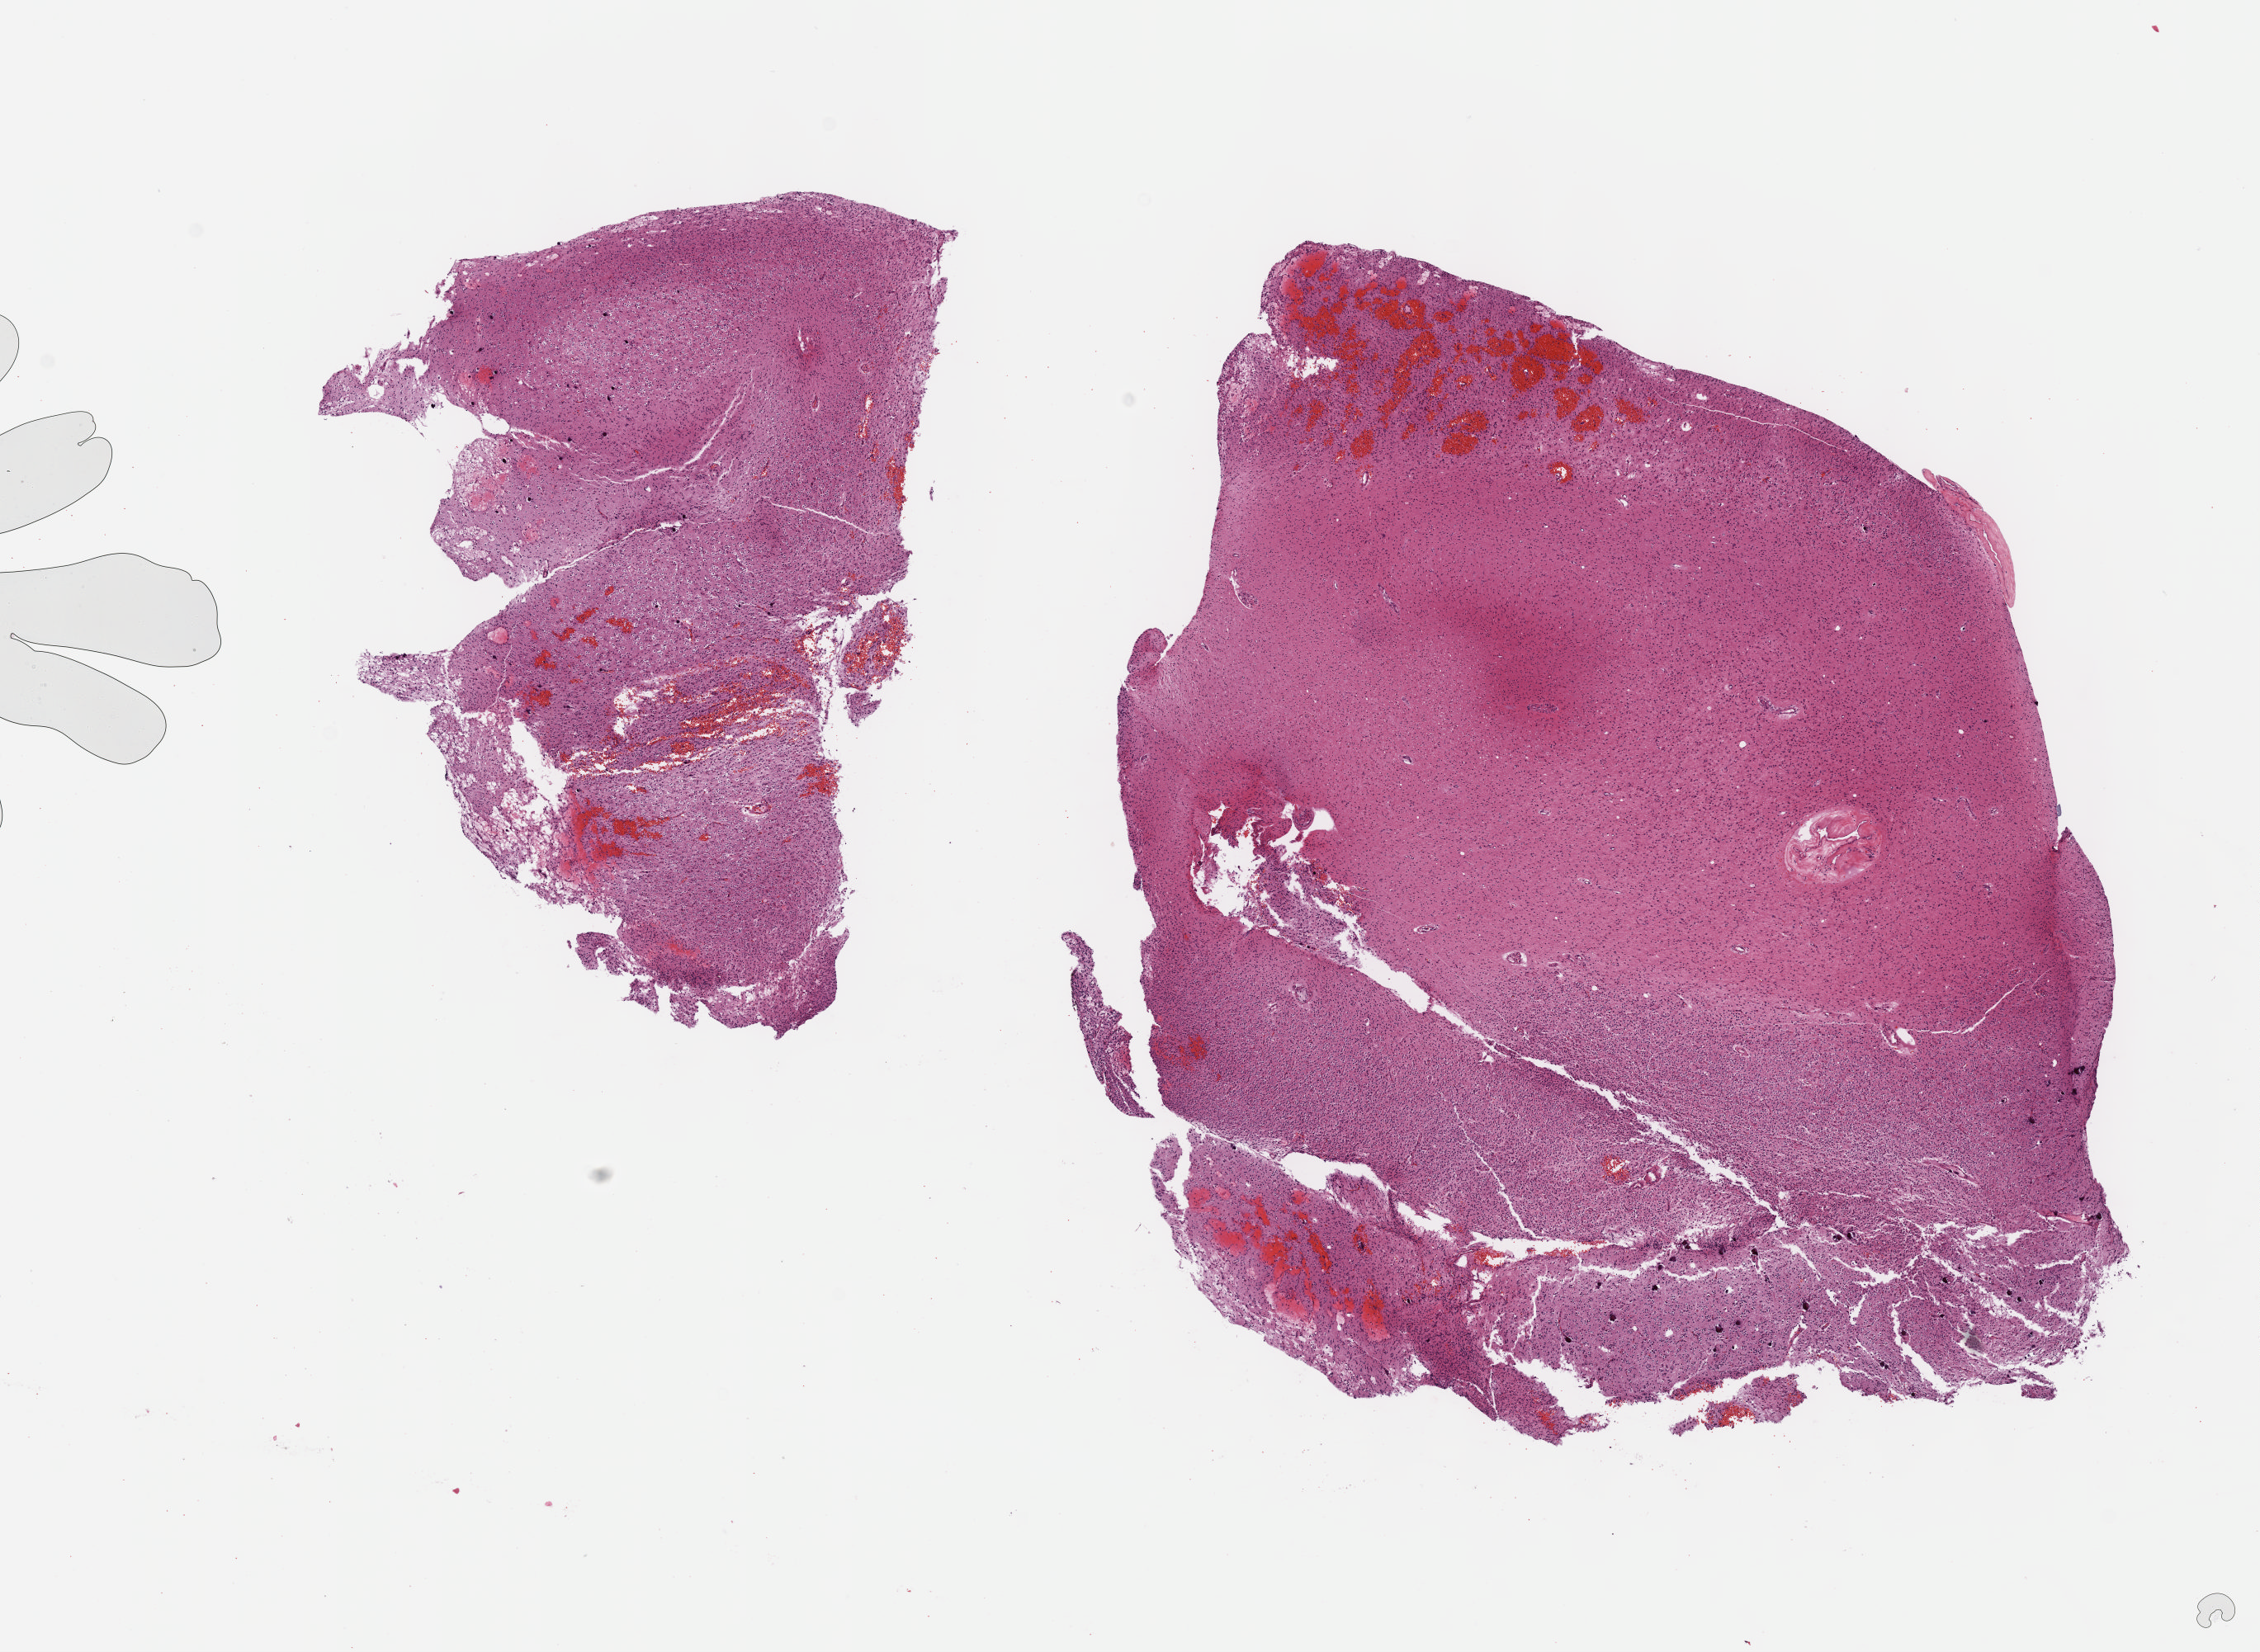
Digitized H&E tissue section (whole slide) — whole scanned area (about 11.1 x 8.1 mm) shown as a low-resolution overview. FFPE section. Brain, primary tumour sample. Male patient; age at initial diagnosis 53 years. Histologic grade: G3 (poorly differentiated).
• histologic diagnosis: Oligodendroglioma, anaplastic (cerebrum)